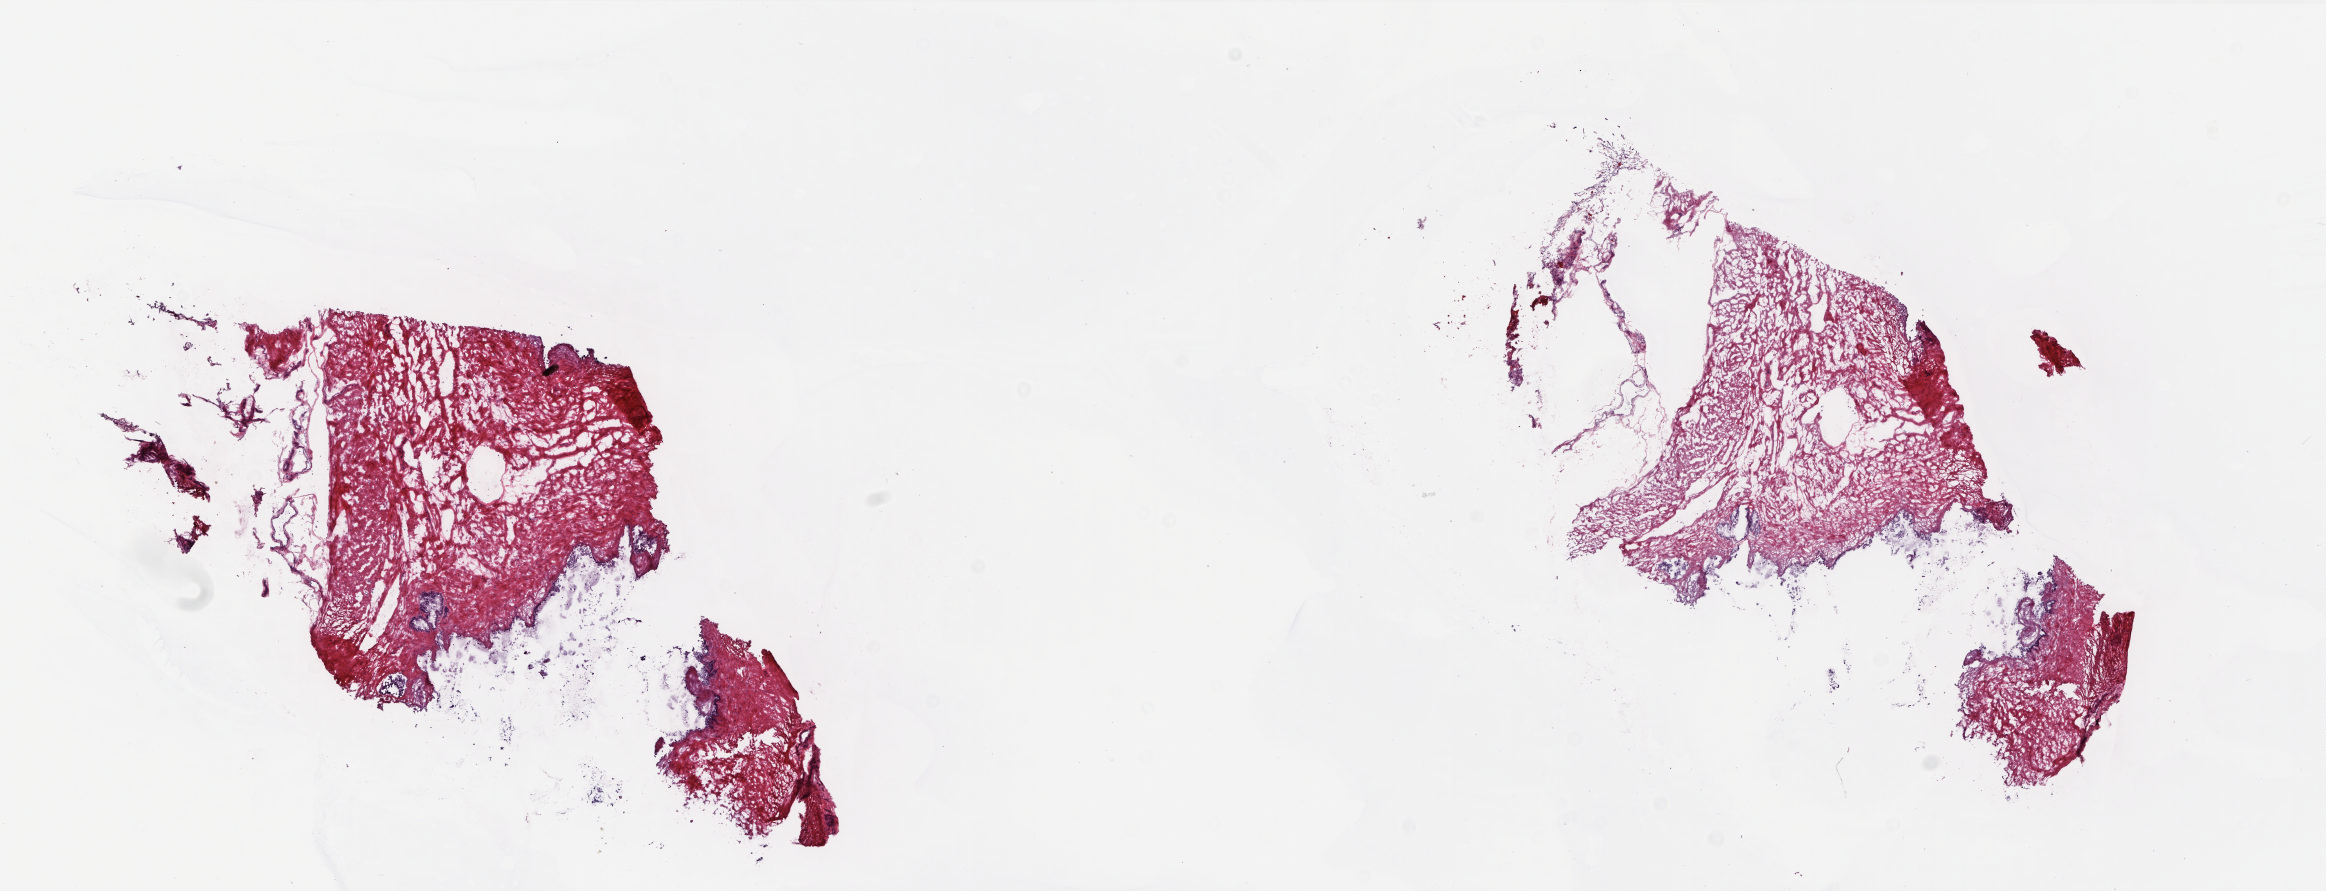
H&E whole-slide image — low-resolution overview of the scanned area, about 18.8 x 7.2 mm, frozen section, solid tissue normal (non-tumour tissue) sample from the prostate. Male, age 69 years at initial diagnosis. Pathologist review of this section (percent, as recorded): tumour cells 0%, tumour nuclei 0%, normal cells 4%, stromal cells 96%, necrosis 0%. Infiltration values recorded for this section: lymphocyte infiltration 2%, monocyte infiltration 0%, neutrophil infiltration 0%.
This section: solid tissue normal sample (biorepository sample class). Patient diagnosis: Adenocarcinoma, NOS (prostate gland).